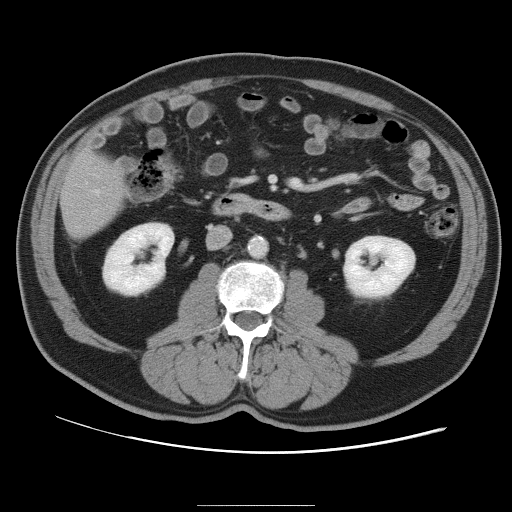
Contrast-enhanced abdominal CT, one axial slice. Slice 27 of 105 in the series (ordered by position). 120 kVp. Intravenous contrast given. Soft-tissue window (W 400 / L 40 HU). 5 mm slice thickness. 512 × 512 image matrix. Male patient, age 64 years. Case-level facts recorded for this patient, not image findings: diagnosis: colorectal cancer liver metastases, imaged before liver resection; multiple liver metastases: yes; largest metastasis: 3 cm; chemotherapy before resection: yes.
Annotated regions visible in this slice (expert manual segmentation):
- hepatic veins: box from (x=95, y=190) to (x=99, y=193) px
- liver: (x=63, y=155)–(x=124, y=237)
- planned liver remnant (the part of the liver to remain after resection): (x=63, y=156)–(x=124, y=229)